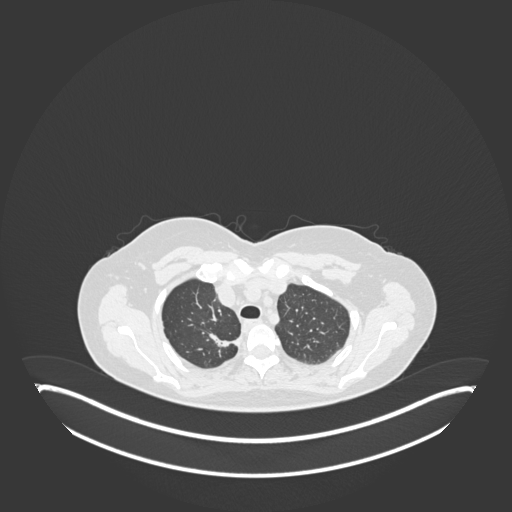
Chest CT, one axial slice; position 145 of 181 along the scan axis; reconstruction kernel B30f; 120 kVp; lung window (W 1500 / L -600 HU); 1 mm slice thickness; 512 × 512 image matrix, field of view 500 × 500 mm. Female patient, age 65 years. Case-level facts recorded for this patient, not image findings: clinical TNM (as recorded): T1b N0 M0.
Structures marked on this image (rectangle marked by the reading radiologist):
- lung tumour (recorded histology: adenocarcinoma): bounding box <204,328,243,352> (left, top, right, bottom; pixels)